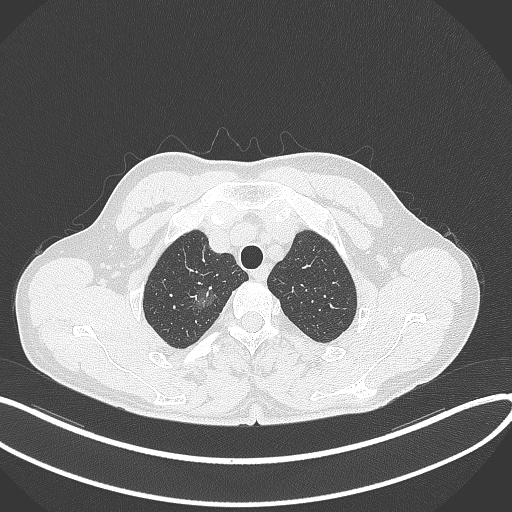
Chest CT, one axial slice; slice 327 of 407 in the series (ordered by position); reconstruction kernel B70f; 120 kVp; lung window (W 1500 / L -600 HU); 1 mm slice thickness; 512 × 512 image matrix, field of view 400 × 400 mm. Male patient, age 58 years. Case-level facts recorded for this patient, not image findings: clinical TNM (as recorded): T1c N0 M0; histopathological grade: G1-2.
Annotated regions visible in this slice (rectangle marked by the reading radiologist):
- lung tumour (recorded histology: adenocarcinoma): bounding box <184,279,219,322> (left, top, right, bottom; pixels)